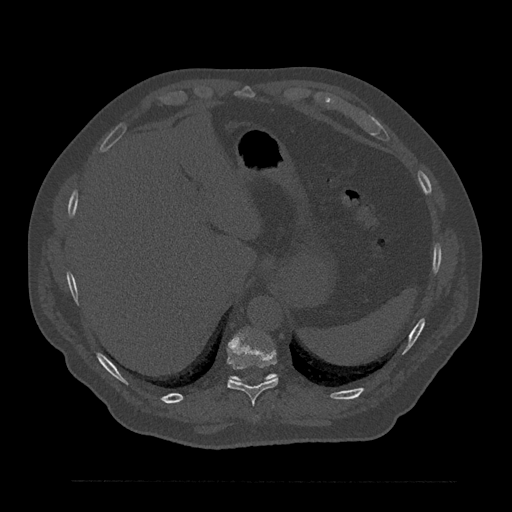
CT including the spine, one axial slice. Slice 336 of 797 in the series (ordered by position). Reconstruction kernel Br40s/3. 120 kVp. Bone window (W 1800 / L 400 HU). 512 × 512 image matrix. Male patient, age 61 years. Case-level facts recorded for this patient, not image findings: primary cancer: prostate.
Annotated regions visible in this slice (semi-automatic segmentation, software-assisted and operator-edited):
- T10 vertebra: bounding box <227,331,279,405> (left, top, right, bottom; pixels)
- T11 vertebra: <230,374,276,382>